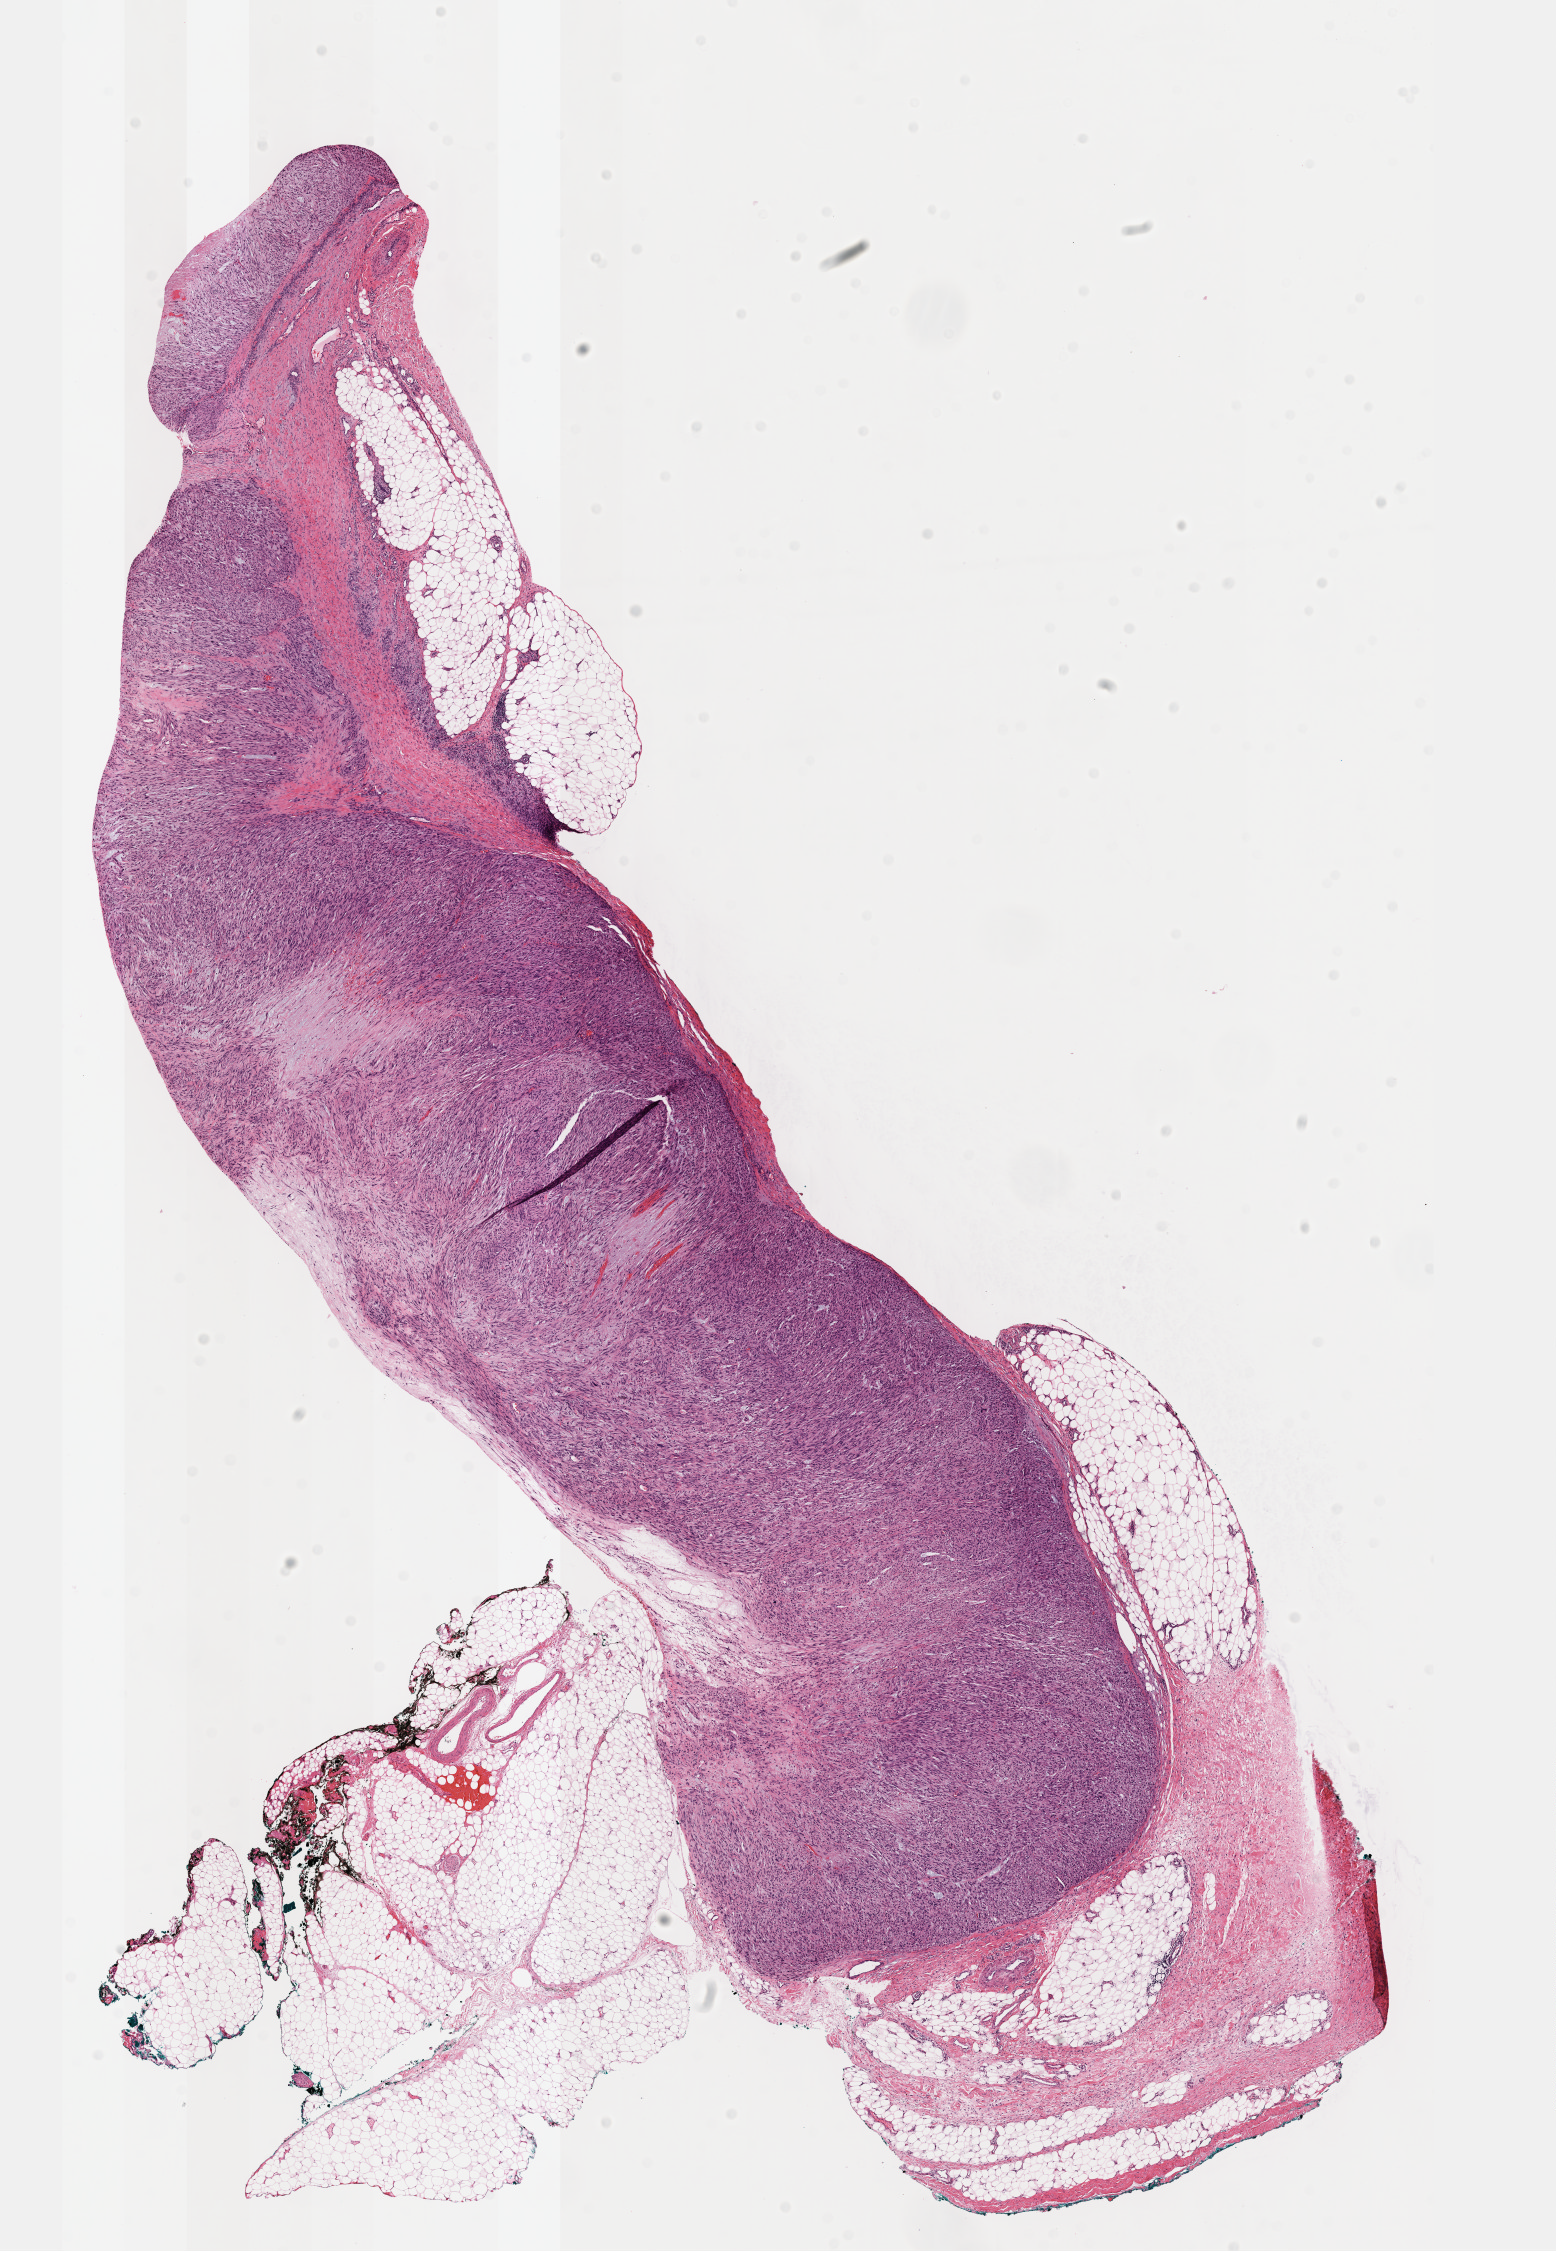
Whole-slide histology image, H&E, a low-resolution overview of the entire scanned area, about 12.6 x 18.2 mm; formalin-fixed paraffin-embedded (FFPE) diagnostic section; primary tumour sample from the connective, subcutaneous and other soft tissues. Female, age 63 years at initial diagnosis.
• histologic diagnosis: Leiomyosarcoma, NOS